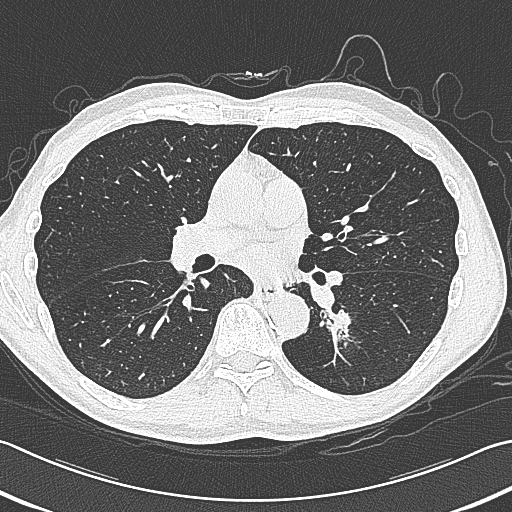
Low-dose screening chest CT, axial slice. Baseline annual screen. Lung window (W 1500 / L -600 HU). 1 mm slice thickness. Lung (sharp) reconstruction kernel (B80f). Male participant, aged 59 years at enrolment.
Expert-annotated lung lesion, bounding box <313,293,375,353> (left, top, right, bottom; pixels). Screening reader's record for this exam (one nodule recorded; not confirmed to be the boxed lesion): non-calcified nodule or mass ≥4 mm, left lower lobe, 15 × 15 mm, smooth margins, soft tissue attenuation. Official screen result: positive, change unspecified: nodule(s) >= 4 mm or enlarging nodule(s), mass(es), or other non-specific abnormalities suspicious for lung cancer. Lung cancer was diagnosed 17 days after this screen: squamous cell carcinoma, large cell, nonkeratinizing, NOS, left lower lobe, poorly differentiated (G3), stage IB (AJCC 6th edition), 31 mm at pathology.